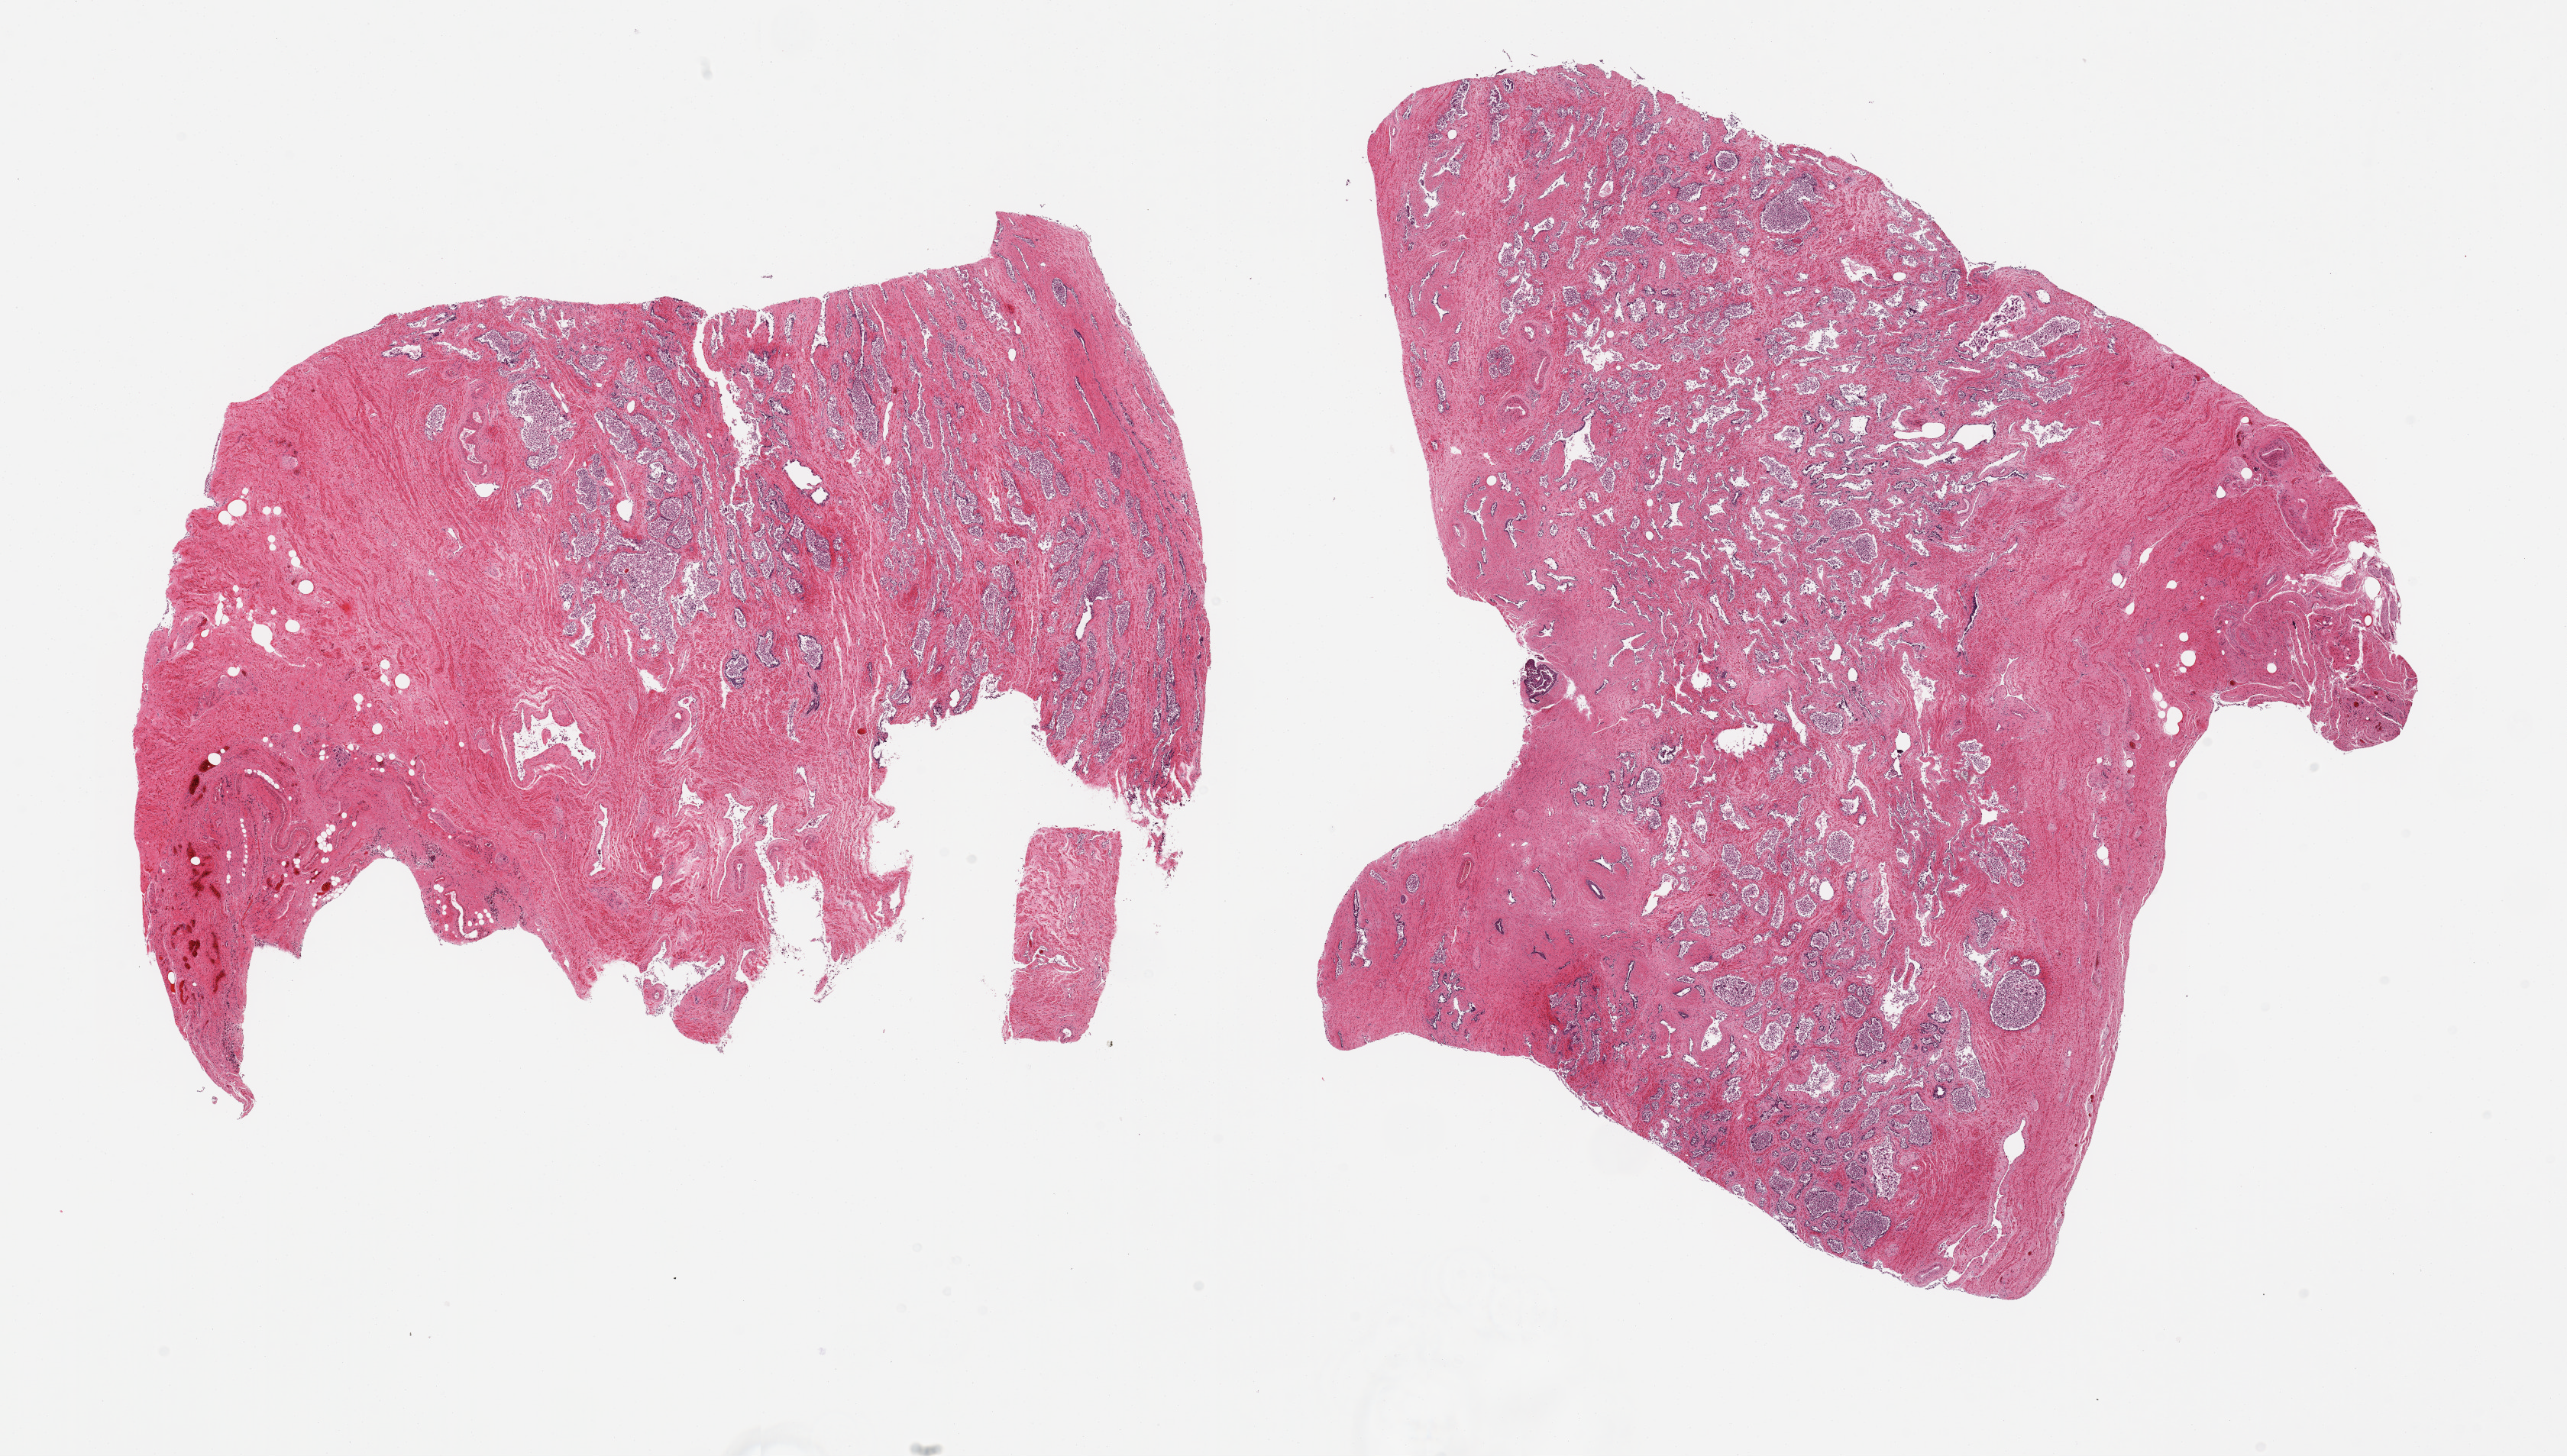
Digitized haematoxylin and eosin-stained section, whole scanned area (about 26.6 x 15.1 mm, acquisition: 20x scan) shown as a low-resolution overview, PAXgene-fixed, paraffin-embedded tissue, sampled site (target tissue): prostate, tissue donor sample.
Pathologist's review note for this sample: 2 pieces, glandular elements with near-total autolysis, sloughed into lumina.